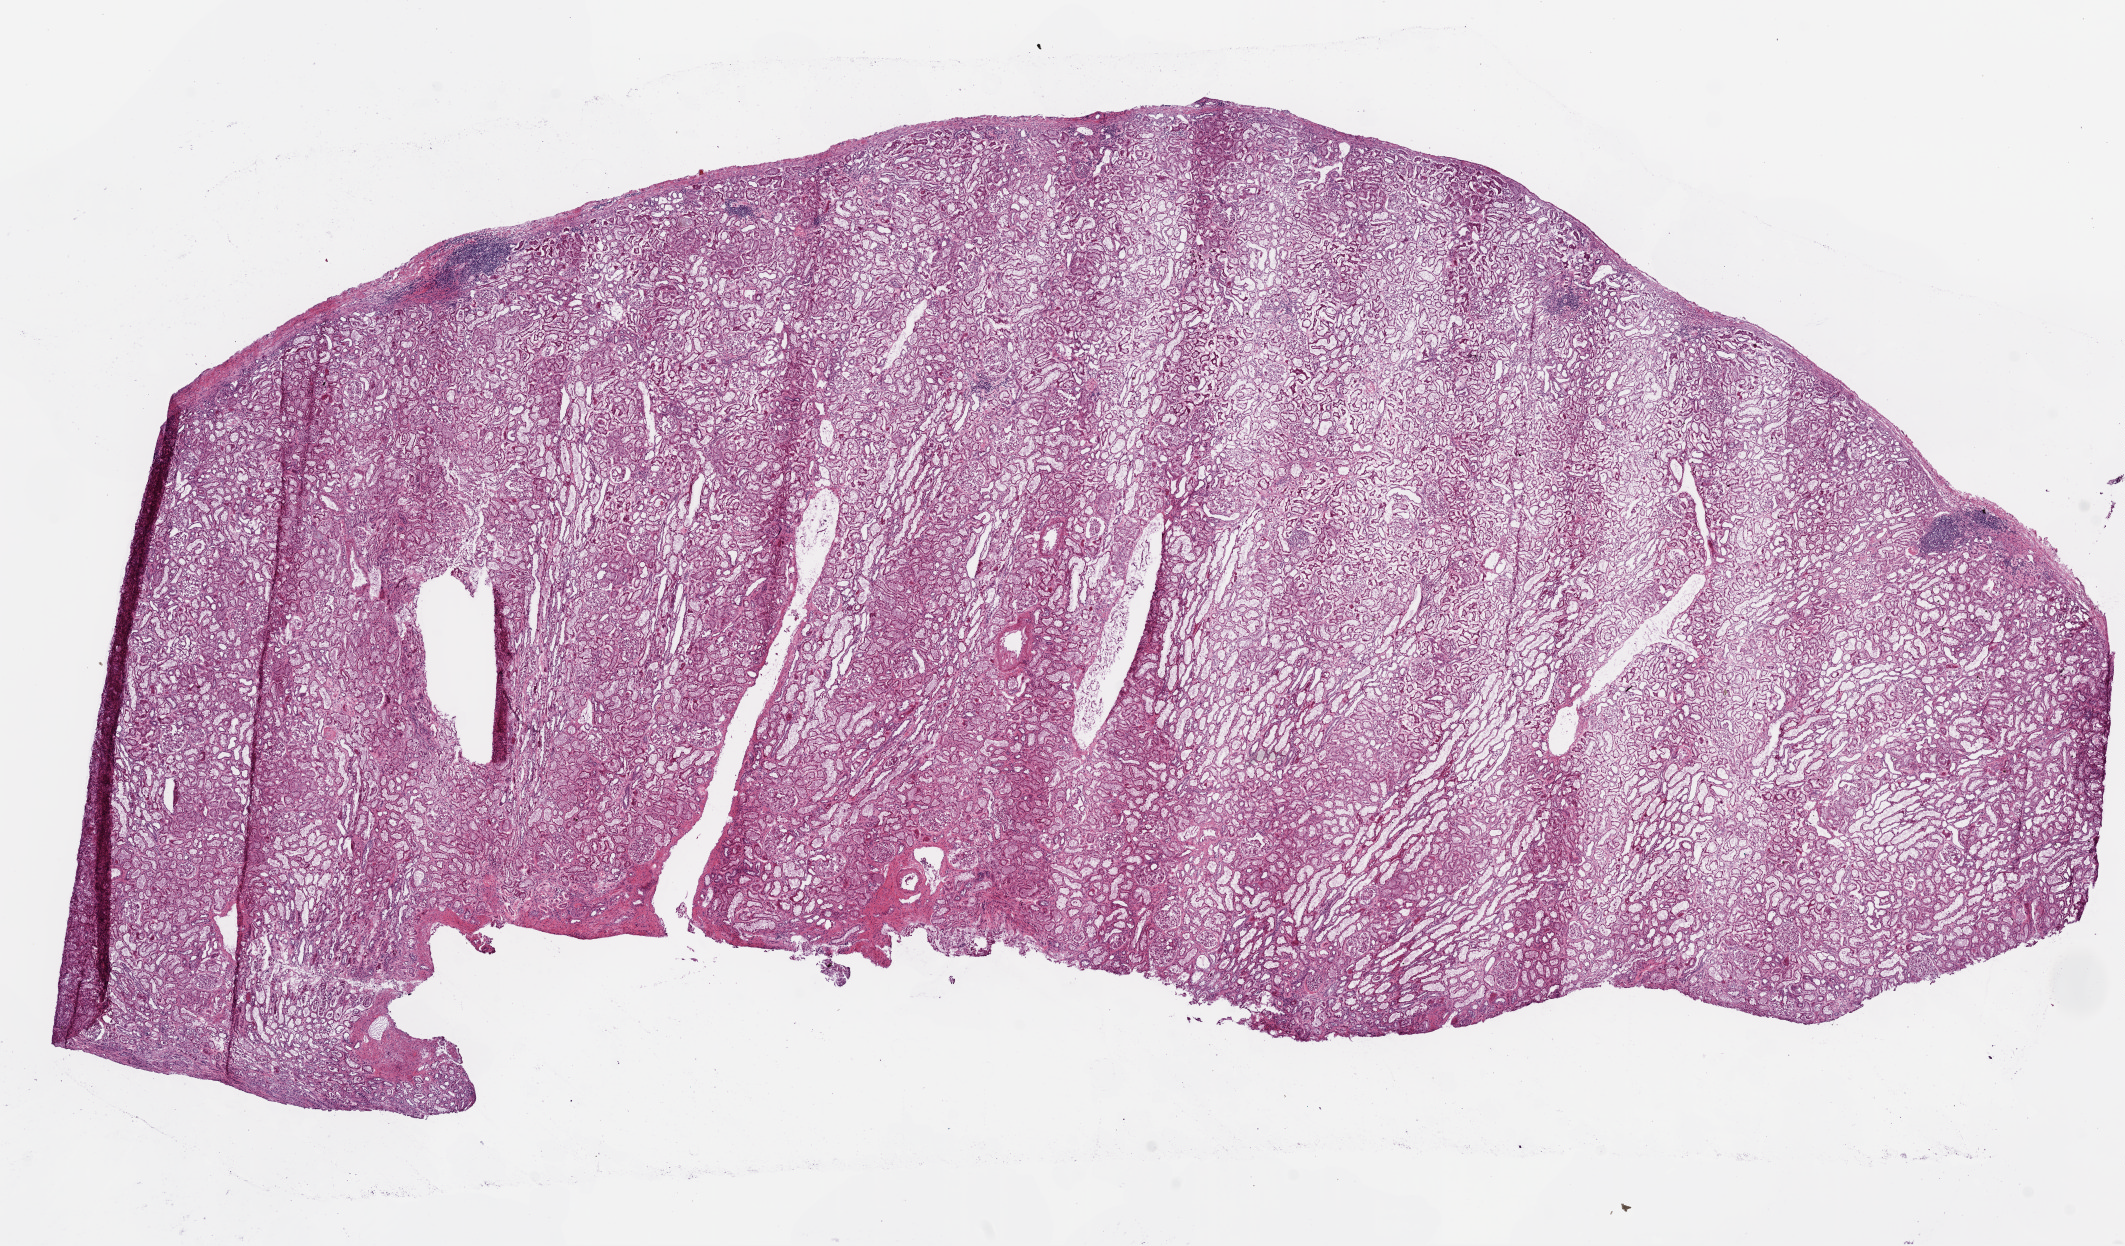
Digitized Hematoxylin and eosin (H&E) stained tissue section (whole slide) — whole scanned area (about 17.1 x 10.0 mm, slide scanned at 20x) shown as a low-resolution overview; frozen section from the bottom of the tissue portion; sample: solid tissue normal (non-tumour tissue), kidney. Female, age 60 years at initial diagnosis.
• this section: solid tissue normal (non-tumour) sample from the same patient
• patient diagnosis: Clear cell adenocarcinoma, NOS